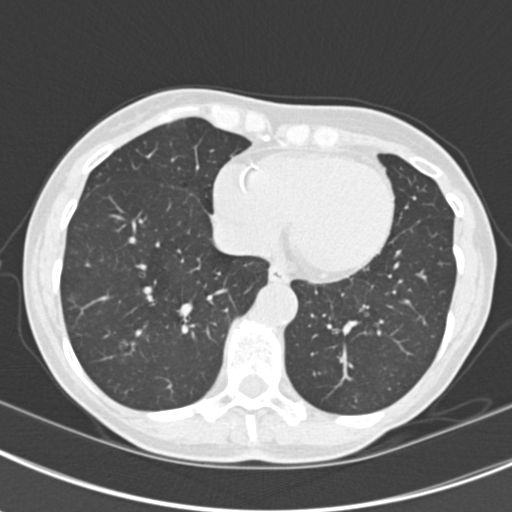
Low-dose screening chest CT, axial slice, second screening round (one year after baseline), lung window (W 1500 / L -600 HU), 2 mm slice thickness, standard (soft-tissue) reconstruction kernel (B30f), slice 137 of 219 in the series, 512 × 512 image matrix, field of view 298 × 298 mm. Female participant, aged 63 years at enrolment.
Lesion marked by an expert reader, bounding box (x1, y1, x2, y2) in pixels: (108, 327, 150, 369). The screening reader recorded 9 non-calcified nodules or masses ≥4 mm on this exam (left upper lobe, right upper lobe, left upper lobe, left lower lobe, right middle lobe, left lower lobe, left lower lobe, right lower lobe, right lower lobe); which of them this box marks is not recorded.